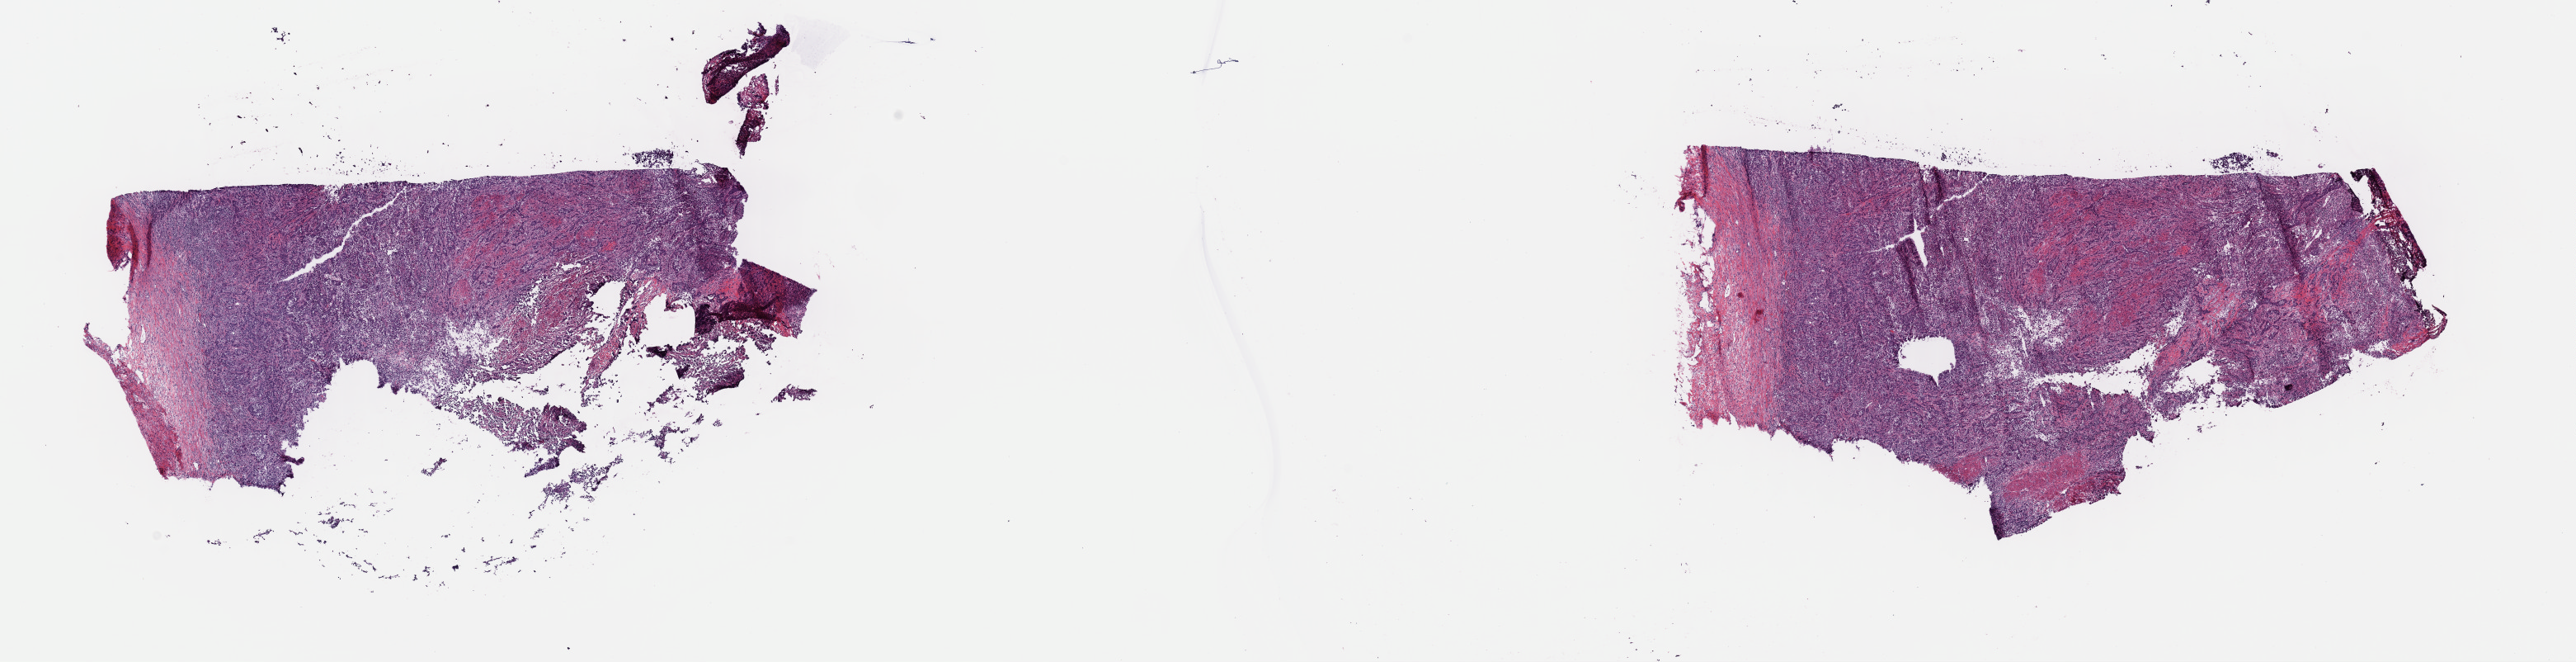
Whole-slide histology image, H&E-stained — low-resolution overview of the scanned area, about 24.7 x 6.3 mm (from a 40x scan), frozen section from the top of the tissue portion, bladder, primary tumour sample. Patient sex: male. Histologic grade: high grade. Slide review estimates, as recorded: tumour cells 80%, tumour nuclei 80%, normal cells 0%, stromal cells 19%, necrosis 1%. Inflammatory infiltration, as recorded: lymphocyte infiltration 4%, monocyte infiltration 1%, neutrophil infiltration 2%.
Lymph nodes positive (case pathology): 0 of 14 examined. AJCC pathologic stage: III (6th edition). Diagnosis: Papillary transitional cell carcinoma (anterior wall of bladder).